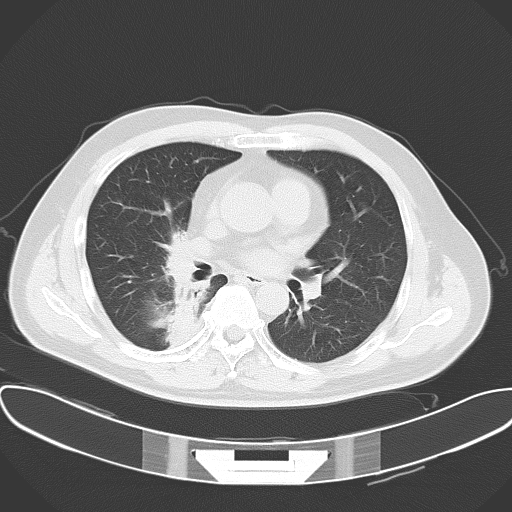
Chest CT, one axial slice; slice 30 of 57 in the series (ordered by position); lung window (W 1500 / L -600 HU); 5 mm slice thickness; 512 × 512 image matrix, field of view 388 × 388 mm. Male patient, age 48 years. From the clinical record (not read from this slice): clinical TNM (as recorded): T1a N1 M1c; histopathological grade: G3.
Annotated regions visible in this slice (bounding box drawn by a radiologist):
- lung tumour (recorded histology: adenocarcinoma): bounding box [x1, y1, x2, y2] px = [163, 230, 213, 348]